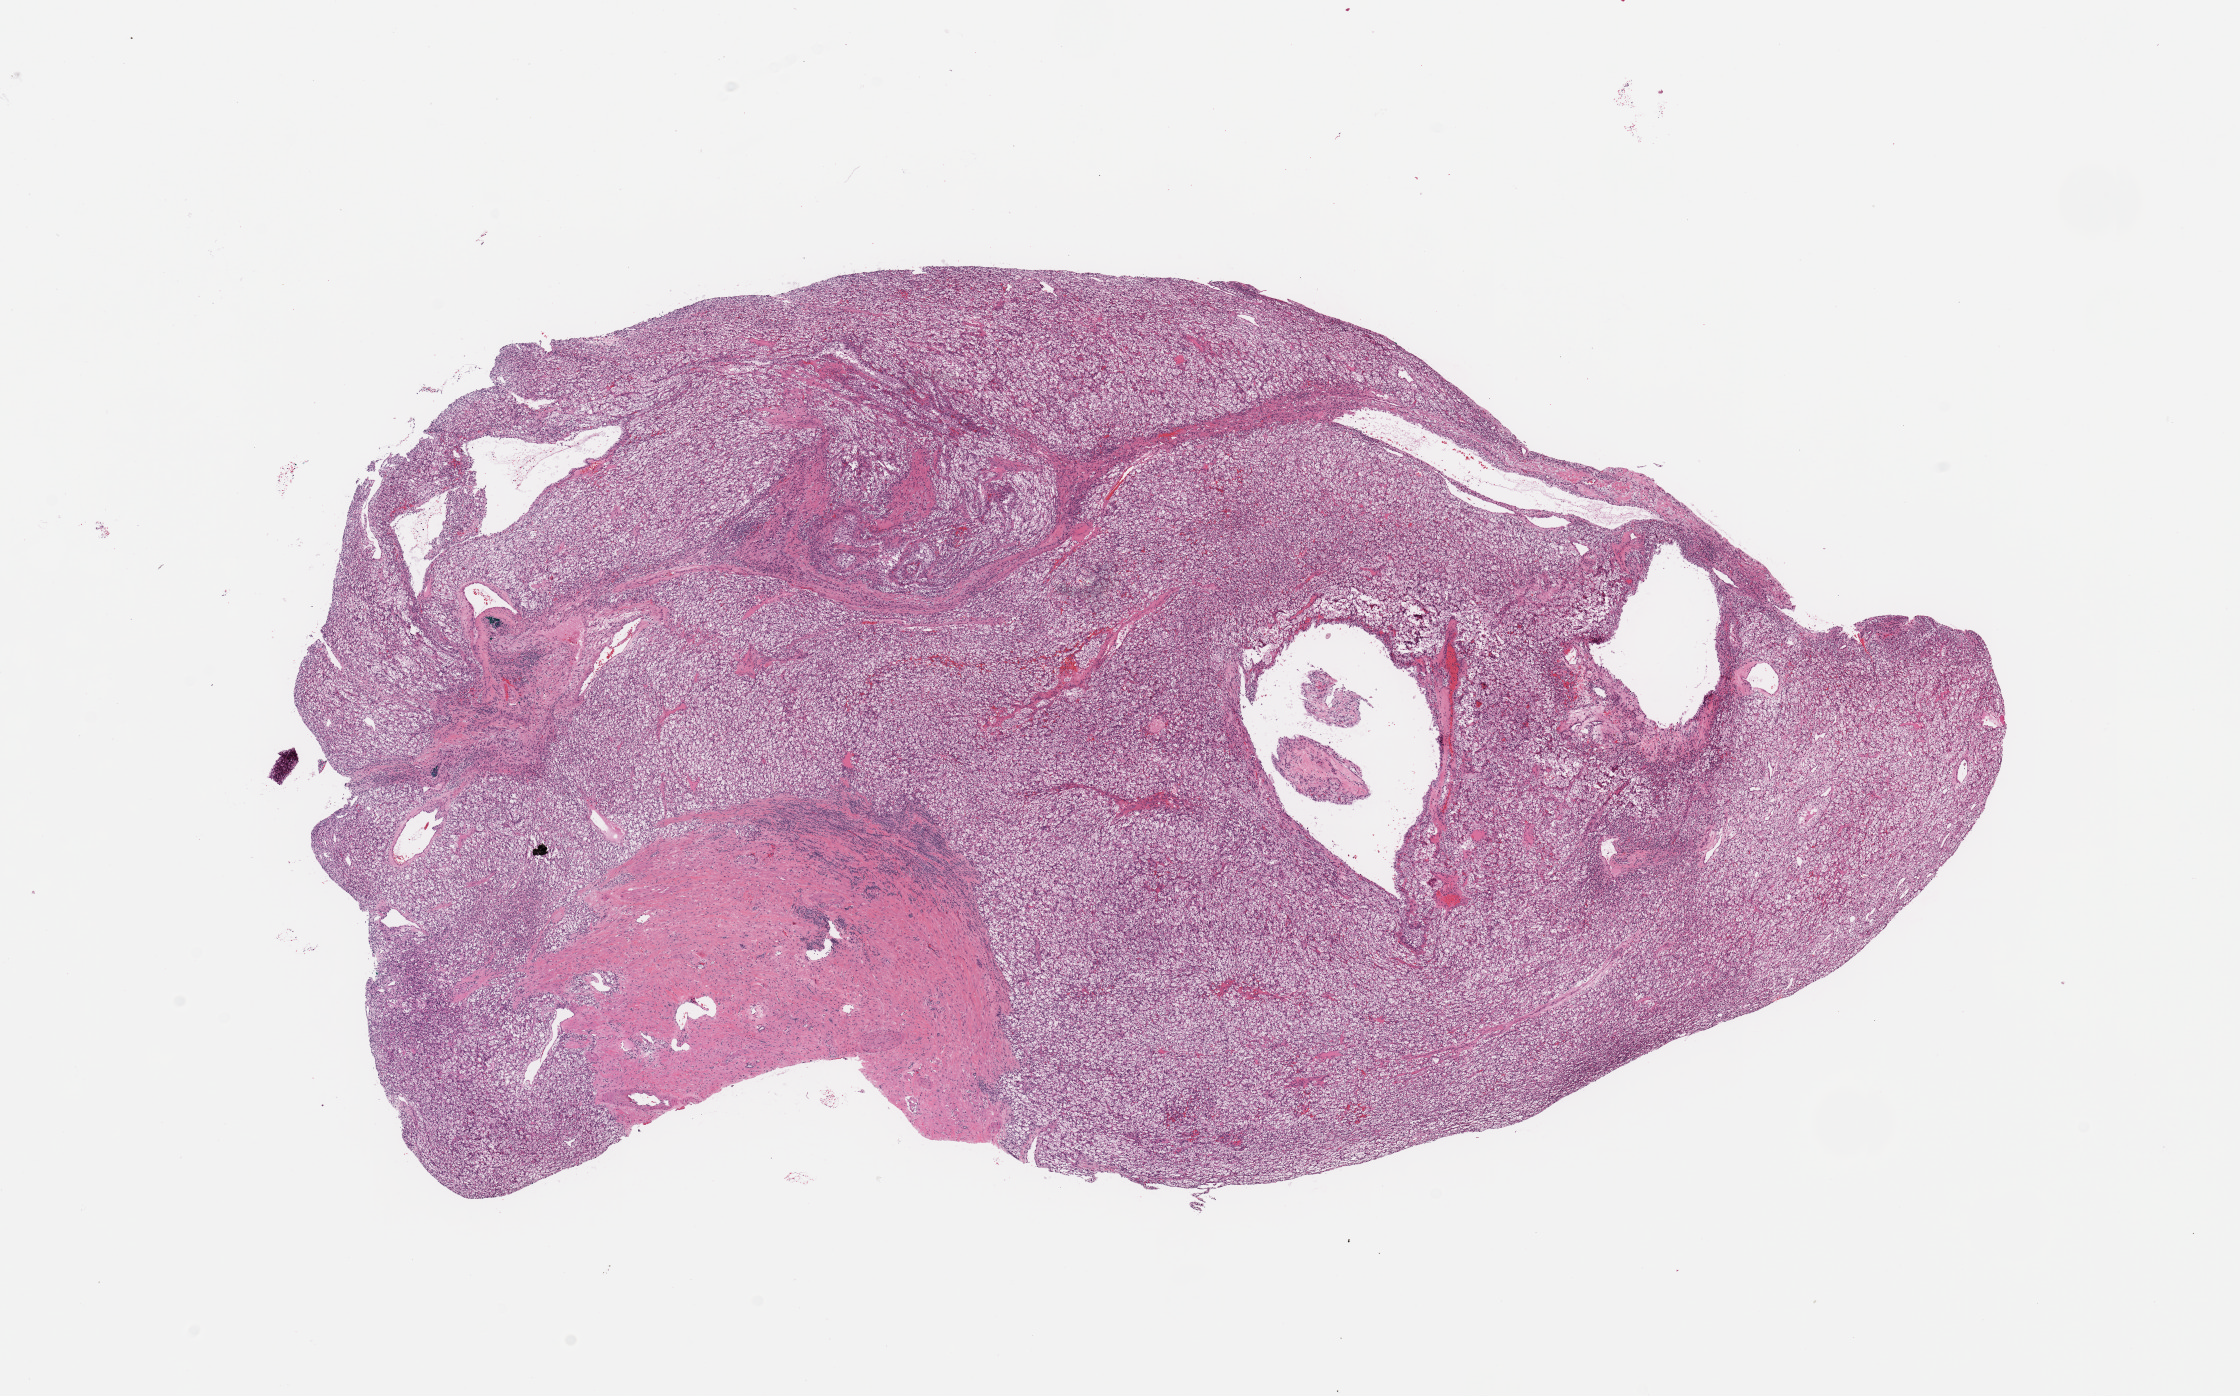
H&E-stained whole-slide image — whole scanned area (about 17.7 x 11.0 mm) shown as a low-resolution overview; kidney, tumour tissue. Female, 59 y/o. Histologic grade: G2 (moderately differentiated).
Diagnosis: Renal cell carcinoma, NOS. AJCC pathologic stage: I. Primary tumour site (as recorded): lower pole.